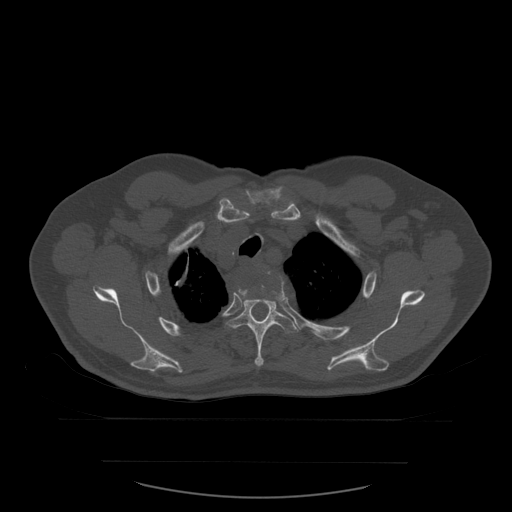
CT including the spine, one axial slice; slice 448 of 590 in the series (ordered by position); bone window (W 1800 / L 400 HU); 512 × 512 image matrix, field of view 479 × 479 mm. Patient age 71 years. From the clinical record (not read from this slice): primary cancer: lung; vertebrae with lytic lesions (as recorded): T1, T2, L5, S1.
Structures marked on this image (semi-automatic segmentation, software-assisted and operator-edited):
- T3 vertebra: bounding box [x1, y1, x2, y2] px = [238, 279, 285, 295]
- T4 vertebra: [226, 283, 298, 367]